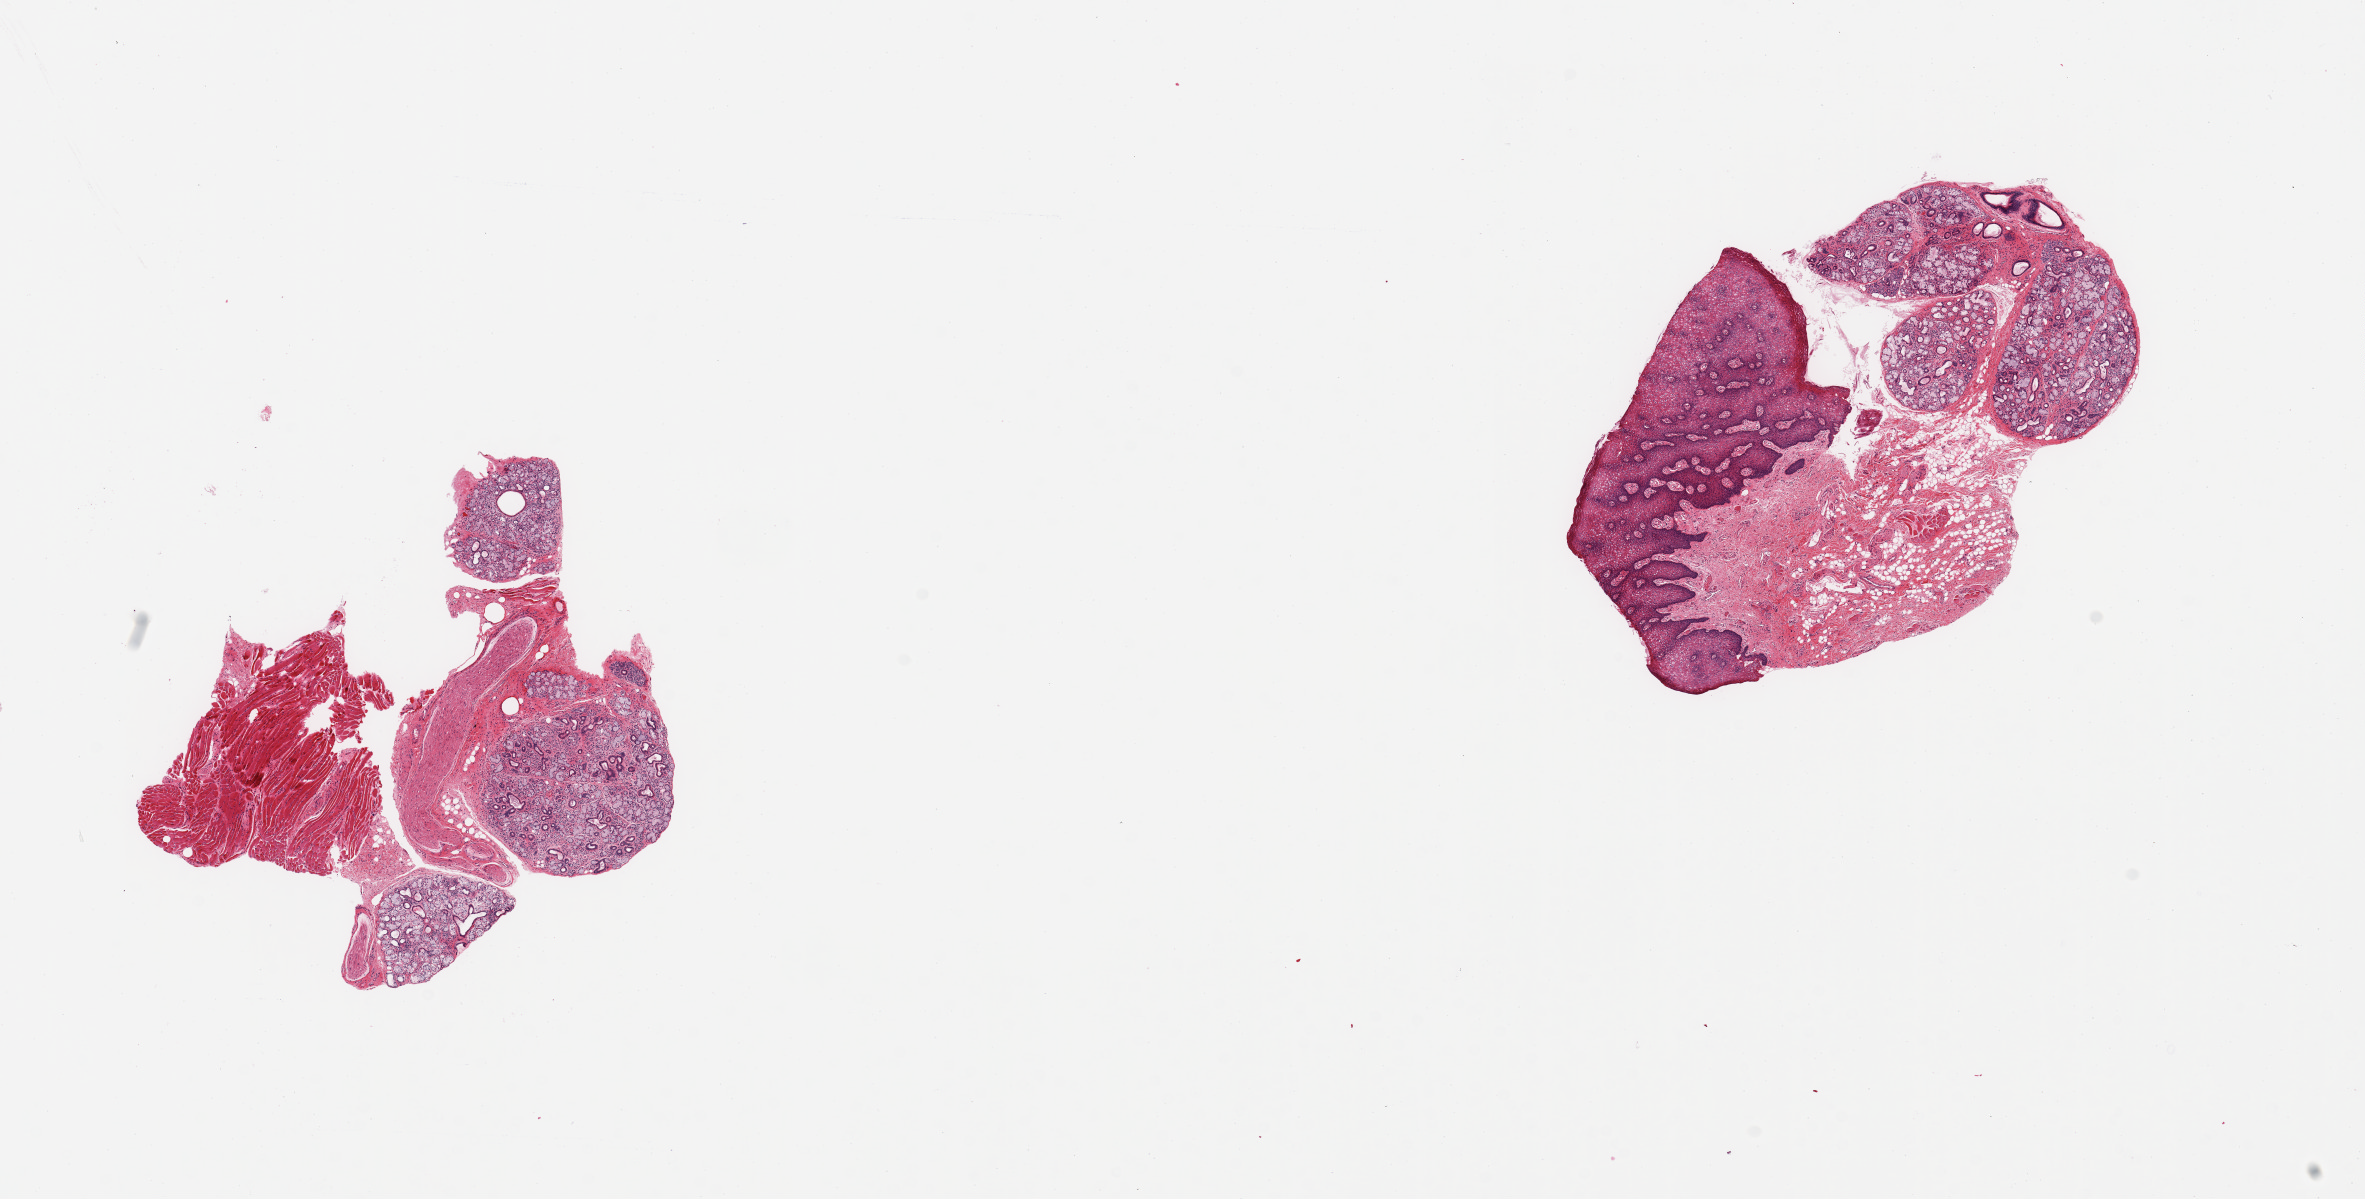
Digitized hematoxylin and eosin (H&E)-stained section, whole scanned area (about 18.7 x 9.5 mm) shown as a low-resolution overview. PAXgene-fixed paraffin-embedded (PFPE) section. Section of minor salivary gland (target tissue). Donor tissue sample. Donor: male.
• reviewer comment on this tissue sample: 2 pieces; well dissected glands, but large amount (50-60%) of extraneous lip, muscle & nerve